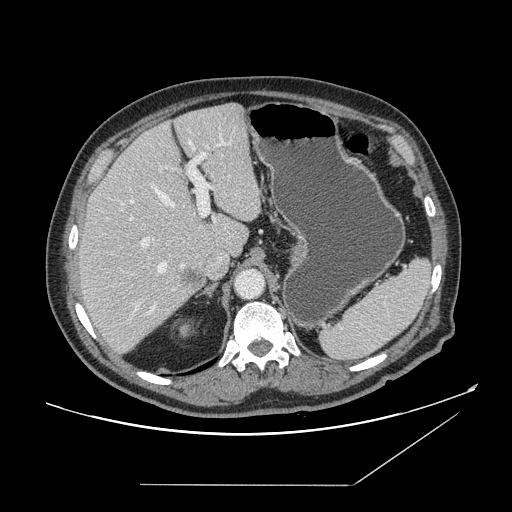
Contrast-enhanced abdominal CT, one axial slice; slice 107 of 166 in the series (ordered by position); soft-tissue window (W 400 / L 40 HU); 2.5 mm slice thickness; 512 × 512 image matrix, field of view 416 × 416 mm. Male patient, age 80 years. Case-level facts recorded for this patient, not image findings: diagnosis: colorectal cancer liver metastases, imaged before liver resection; multiple liver metastases: no; largest metastasis: 2.2 cm; disease in both lobes: no.
Structures marked on this image (outlined manually by an expert reader):
- hepatic veins: box from (x=131, y=140) to (x=193, y=309) px
- liver: (x=79, y=104)–(x=261, y=355)
- planned liver remnant (the part of the liver to remain after resection): (x=87, y=104)–(x=261, y=258)
- portal vein (with intrahepatic branches): (x=131, y=141)–(x=225, y=311)
- liver metastasis: (x=184, y=272)–(x=204, y=291)
- liver metastasis: (x=180, y=269)–(x=205, y=286)